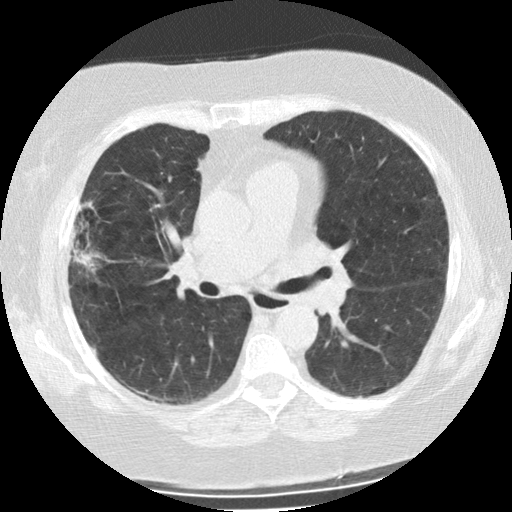
Chest CT (low-dose screening protocol), one axial image. Second screening round (one year after baseline). Lung window (W 1500 / L -600 HU). 2.5 mm slice thickness. Female, age 73 years at enrolment. Former smoker at enrolment.
- Expert-annotated lung lesion, bounding box (x1, y1, x2, y2) in pixels: (57, 201, 106, 276).
- The screening reader recorded 2 non-calcified nodules or masses ≥4 mm on this exam (right upper lobe, left upper lobe); which of them this box marks is not recorded.
- Lung cancer was diagnosed 47 days after this screen: bronchiolo-alveolar adenocarcinoma, NOS, right upper lobe, moderately differentiated (G2), stage IIIB (AJCC 6th edition), 21 mm at pathology.